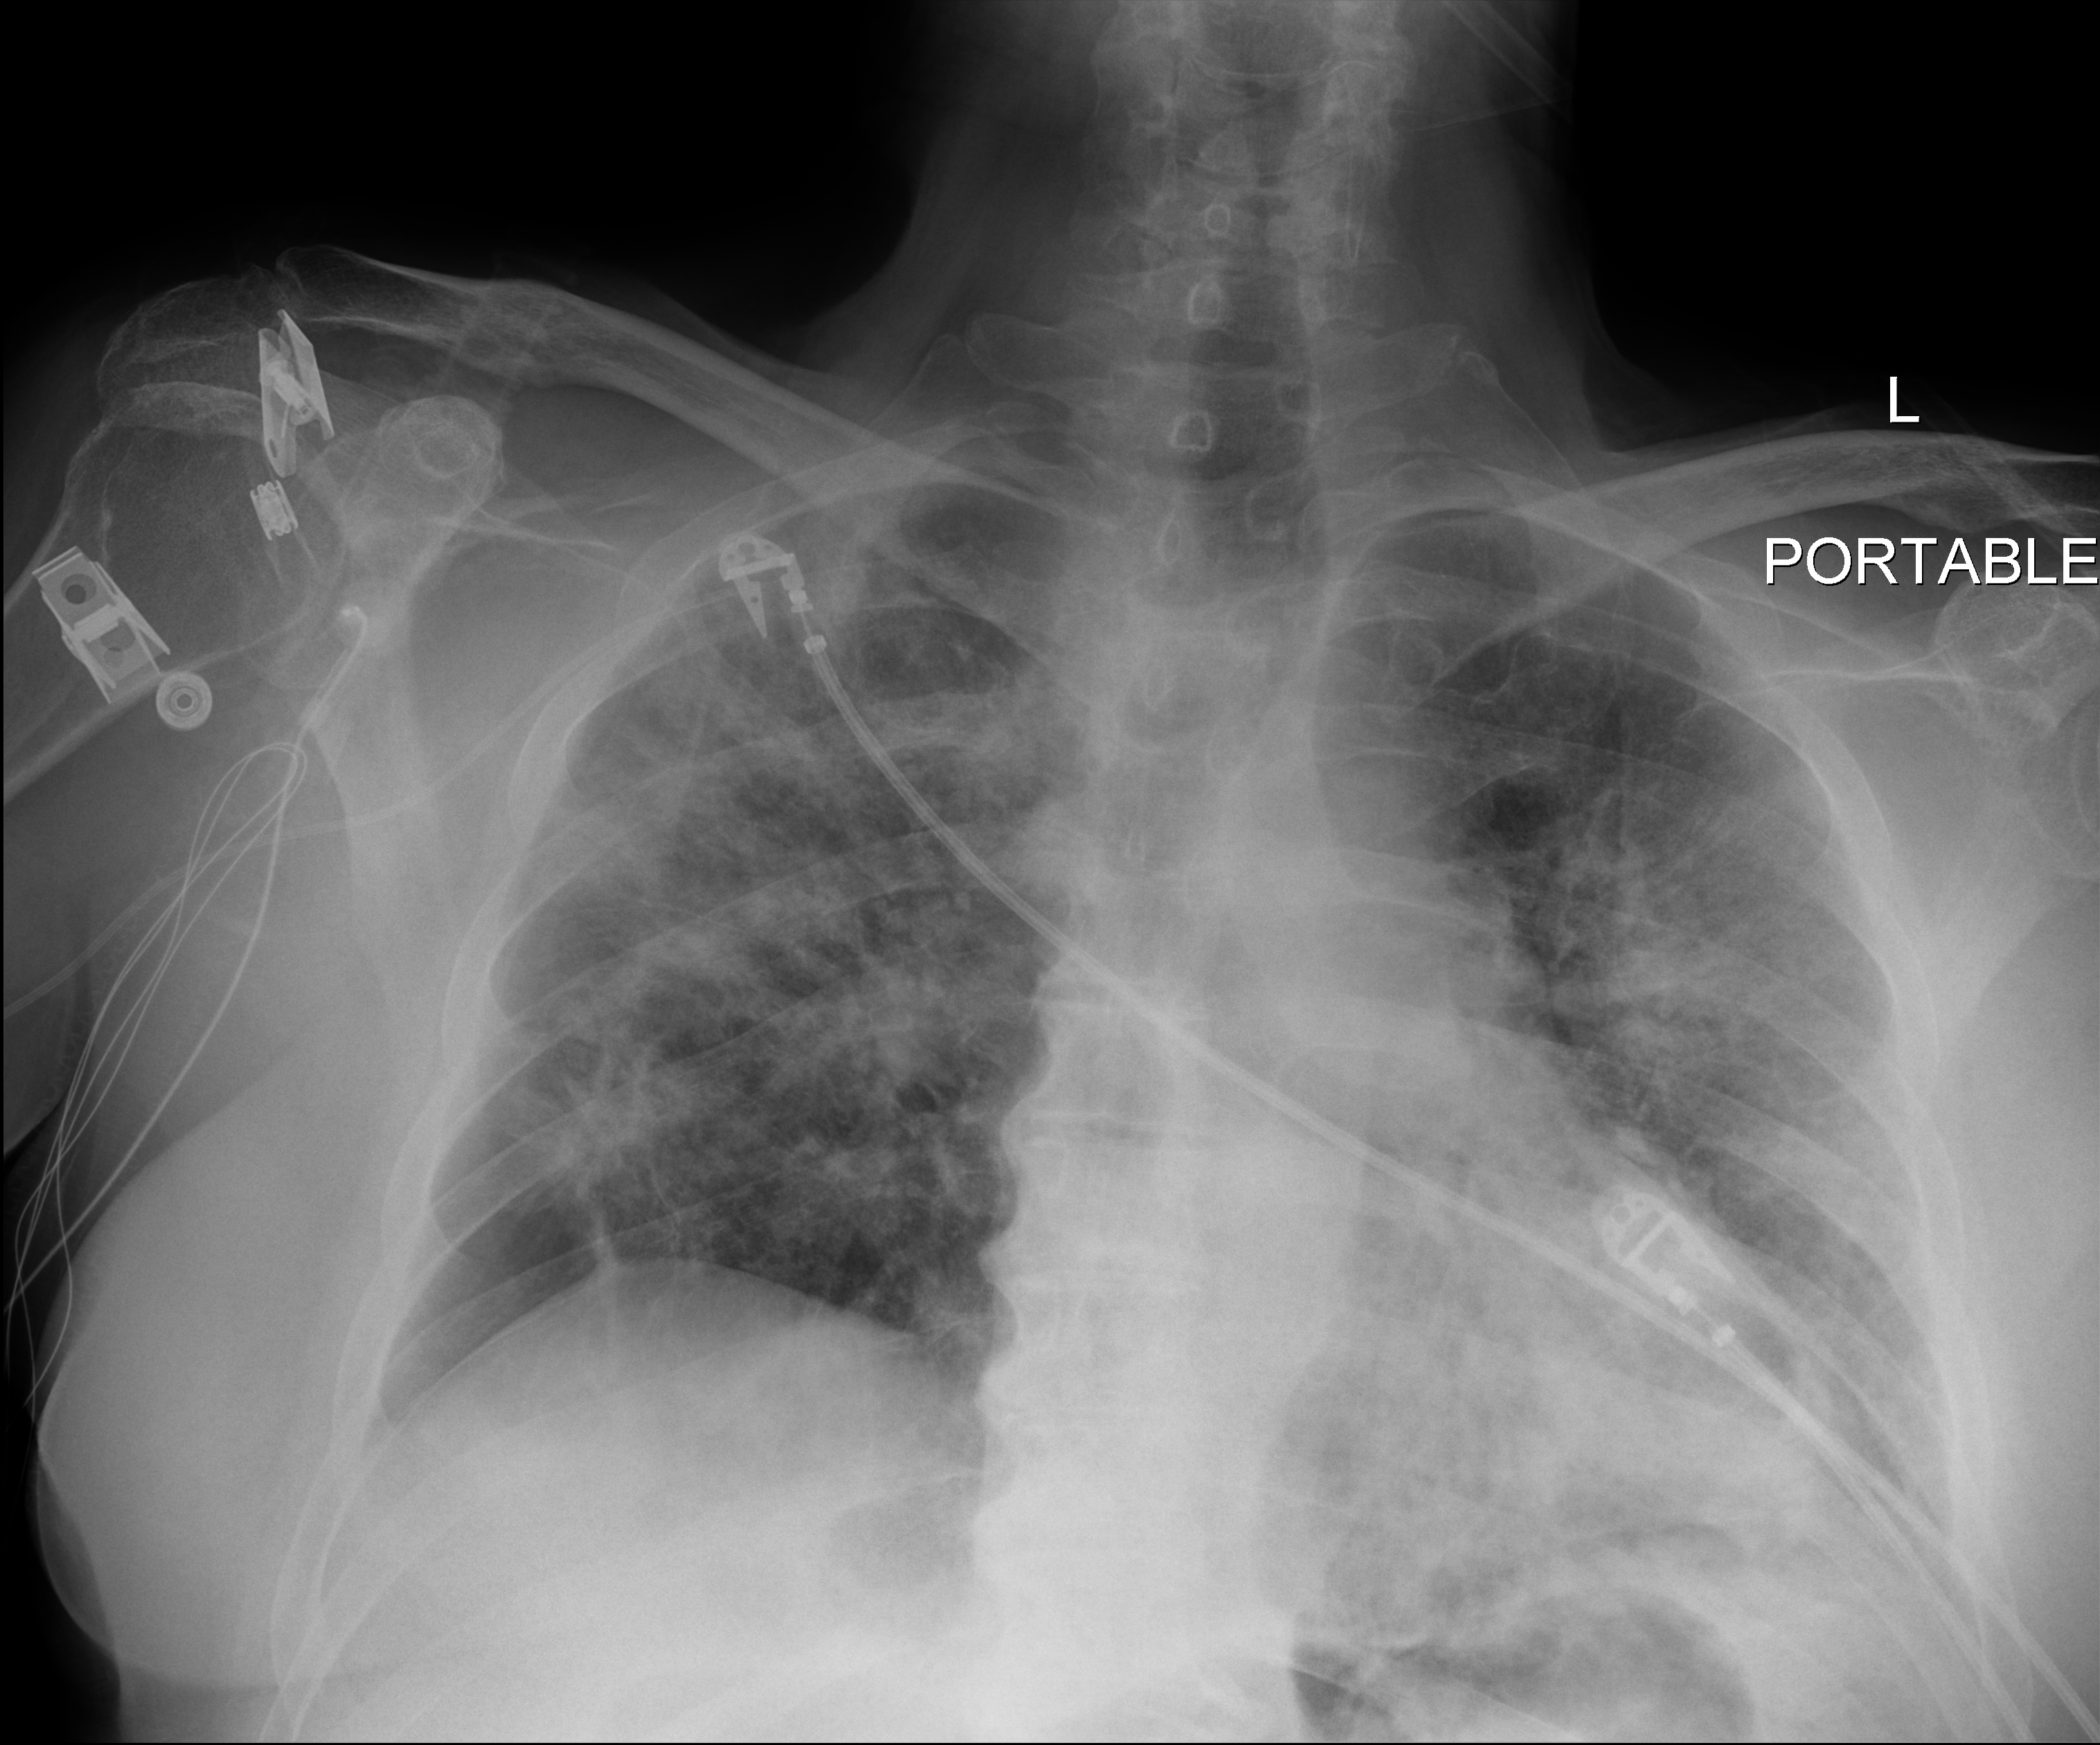
Chest X-ray (portable); anteroposterior (AP) projection. Male patient hospitalised with COVID-19, age 60–74 years.
Hospital-stay facts (about this admission, not read from this image; timing relative to this image not recorded):
- mechanically ventilated during this hospital stay: no